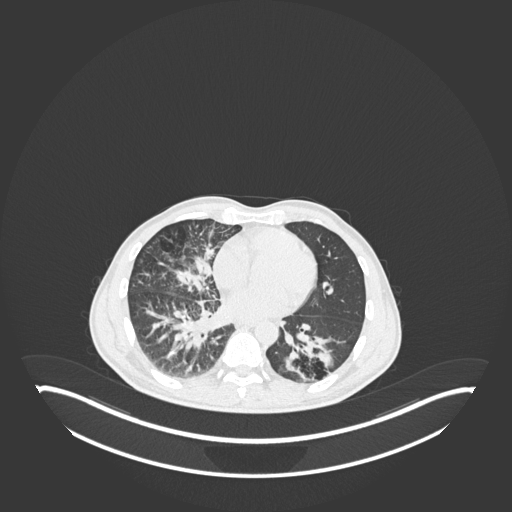
Chest CT, one axial slice; position 99 of 237 along the scan axis; lung window (W 1500 / L -600 HU); 1 mm slice thickness; 512 × 512 image matrix. Male patient, age 49 years. From the clinical record (not read from this slice): clinical TNM (as recorded): T2b N1 M0.
Structures marked on this image (bounding box drawn by a radiologist):
- lung tumour (recorded histology: adenocarcinoma): box from (x=283, y=328) to (x=335, y=382) px